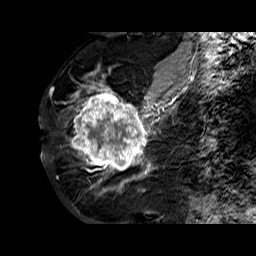
Breast MRI (dynamic contrast-enhanced), one sagittal slice; position 30 of 60 along the scan axis; dynamic contrast-enhanced series, time point 2 of 6 at this slice position (early post-contrast); 1.5 T; TE 6.3 ms, TR 32.4 ms; 4 mm slice thickness; 256 × 256 image matrix, field of view 200 × 200 mm. Female patient. Case-level facts recorded for this patient, not image findings: setting: breast cancer imaged before/during neoadjuvant chemotherapy; receptor status: HR-positive, HER2-negative.
Outlined on this slice (semi-automatically segmented with operator editing):
- analysis volume of interest (the breast-tissue region the enhancement analysis was run in; not a lesion): bounding box [x1, y1, x2, y2] px = [68, 72, 177, 183]
- tumour enhancement mask (voxels above the 100 % enhancement threshold inside the analysis volume of interest): [73, 82, 175, 183]